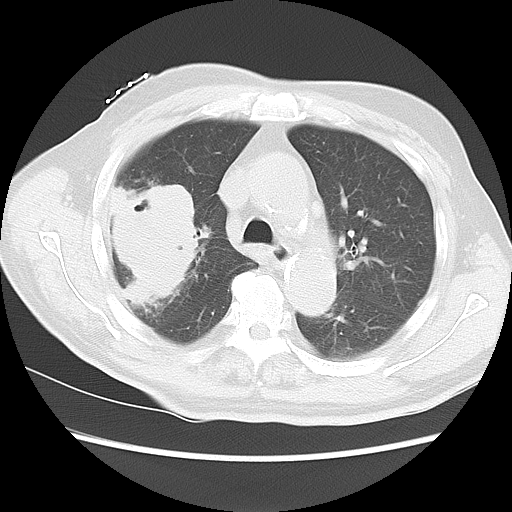
Chest CT, one axial slice; position 11 of 15 along the scan axis; reconstruction kernel LUNG; lung window (W 1500 / L -600 HU); 5 mm slice thickness; 512 × 512 image matrix, field of view 350 × 350 mm. Male patient, age 68 years. From the clinical record (not read from this slice): clinical TNM (as recorded): T4 N3 M0.
Outlined on this slice (bounding box drawn by a radiologist):
- lung tumour (recorded histology: squamous cell carcinoma): bounding box (x1, y1, x2, y2) in pixels: (112, 173, 210, 308)